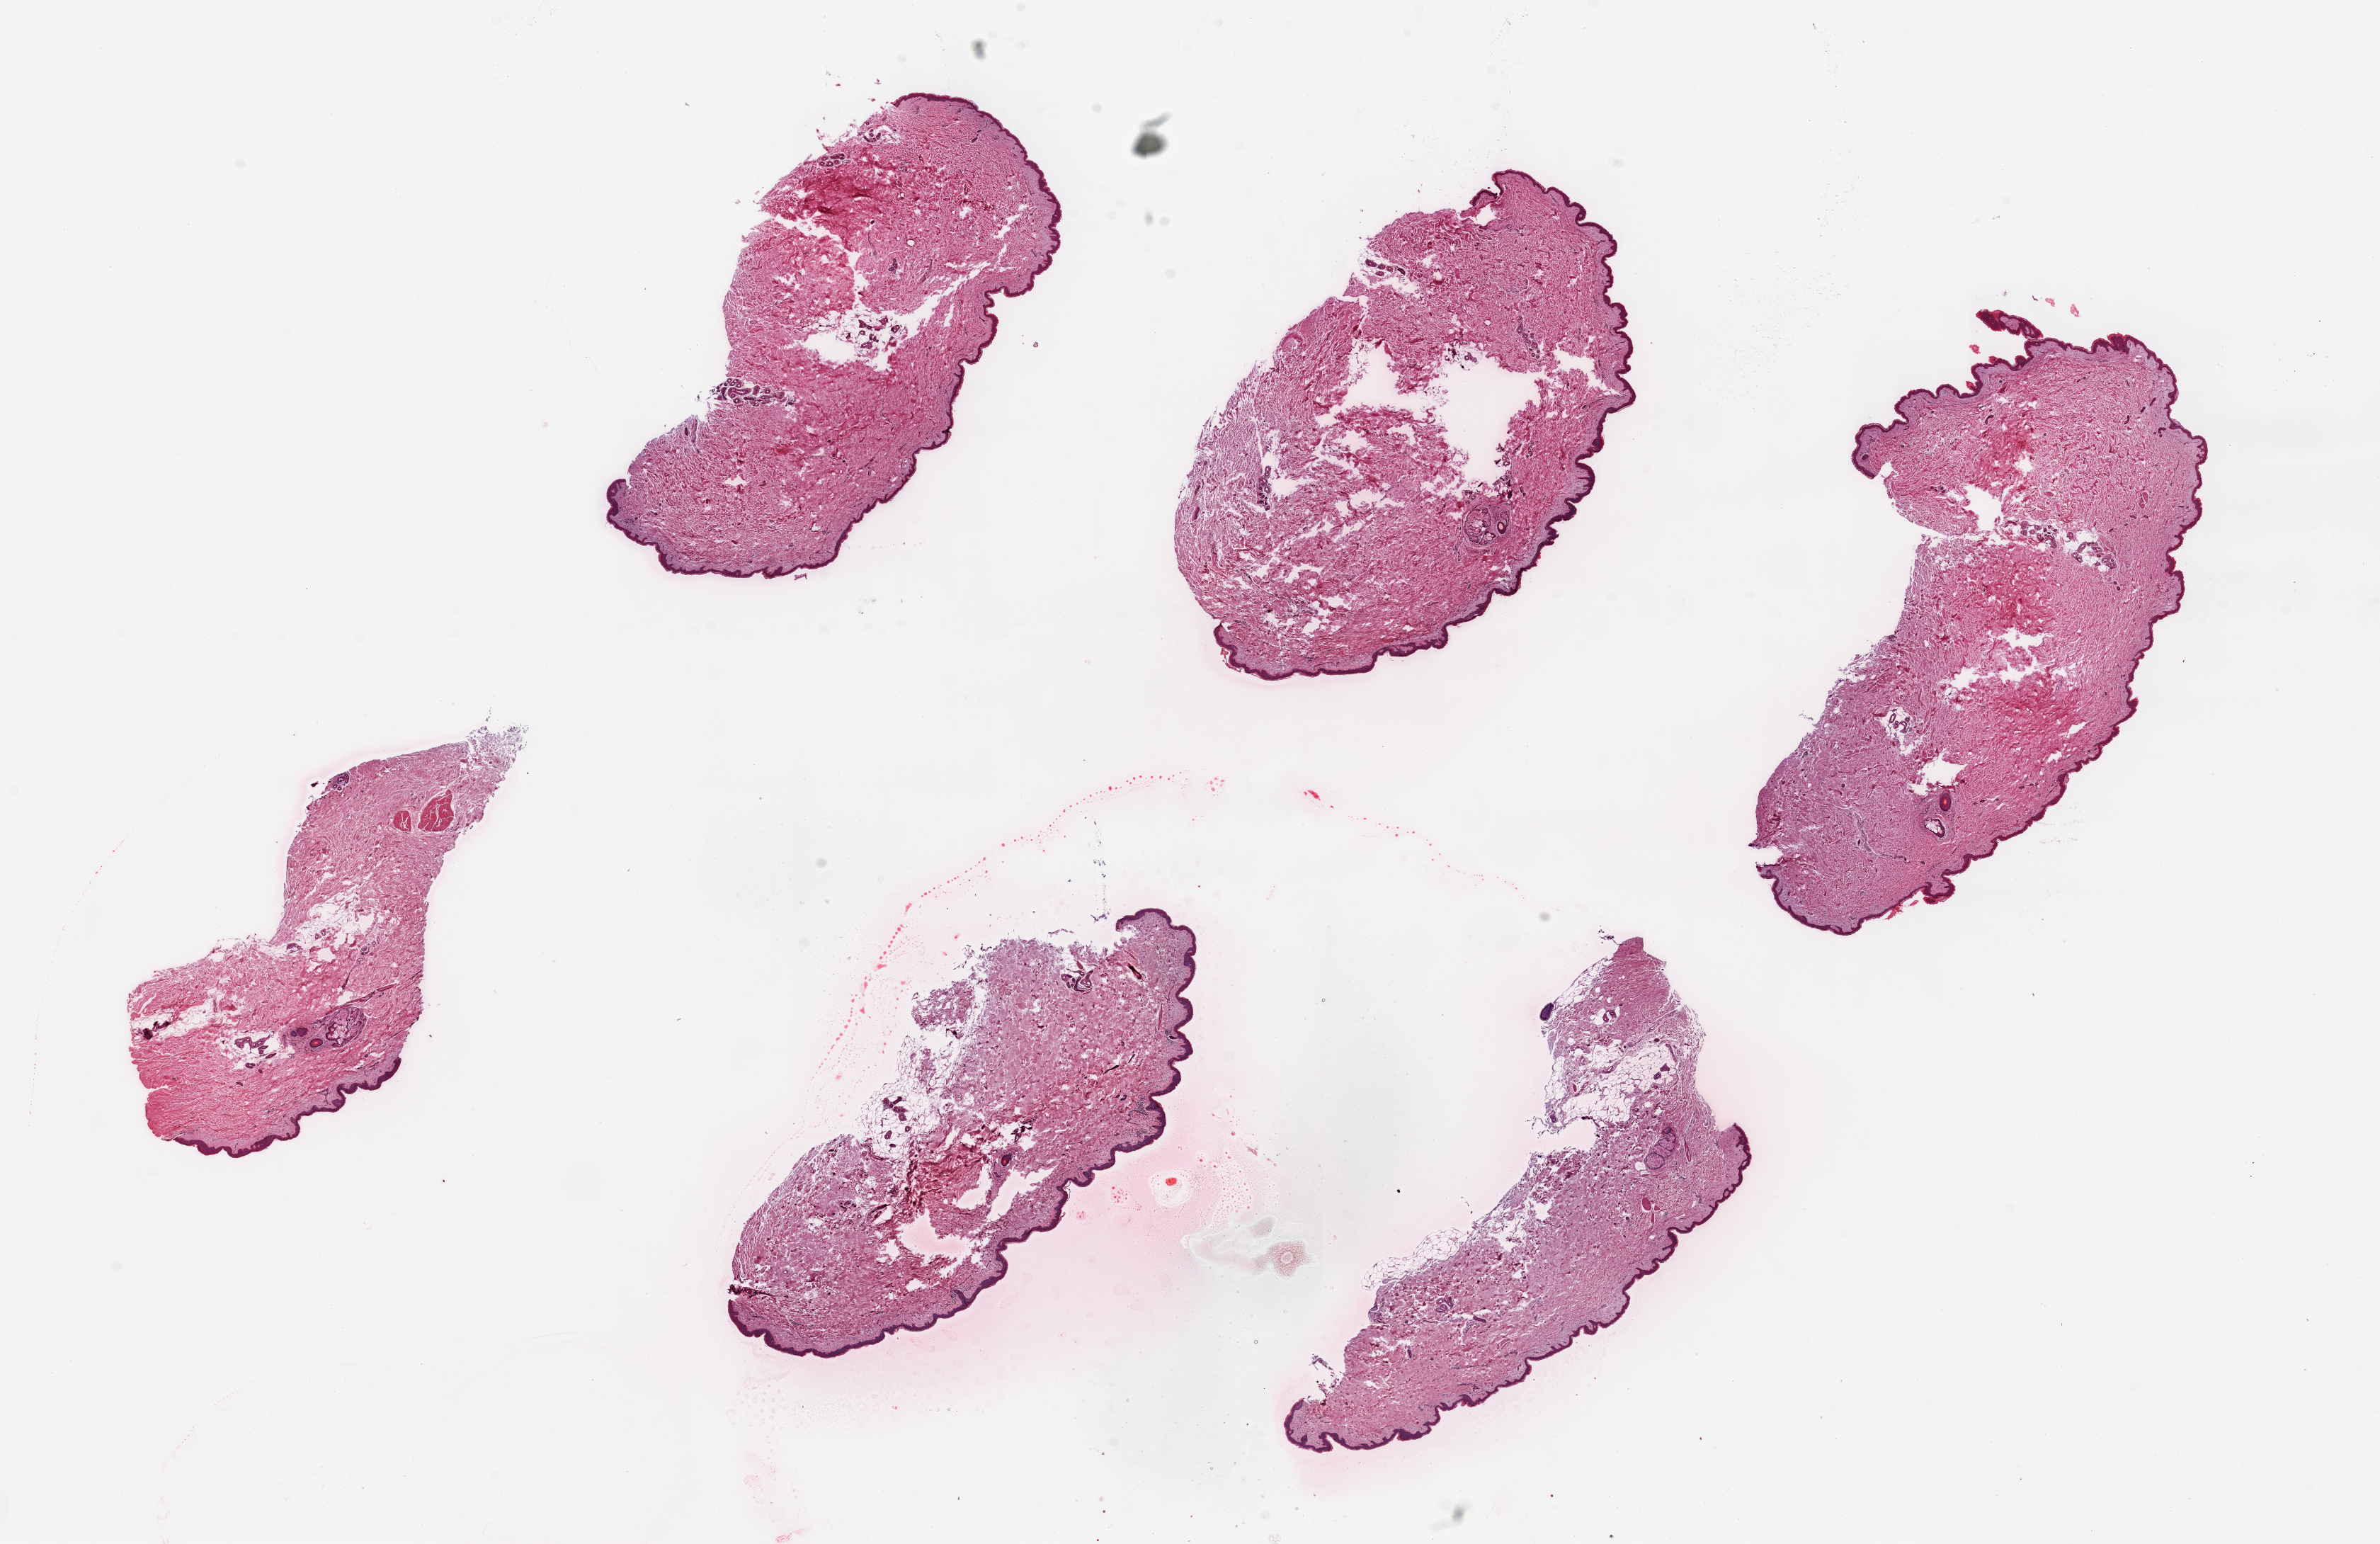
Digitized H&E-stained section, low-resolution overview of the scanned area, about 26.6 x 17.2 mm, PAXgene-fixed paraffin-embedded (PFPE) section, target tissue: skin of suprapubic region, tissue donor sample. Donor: female.
• reviewer comment on this tissue sample: 2 pieces ~7x3mm. Squamous epithelium is < 2-3% of thickness